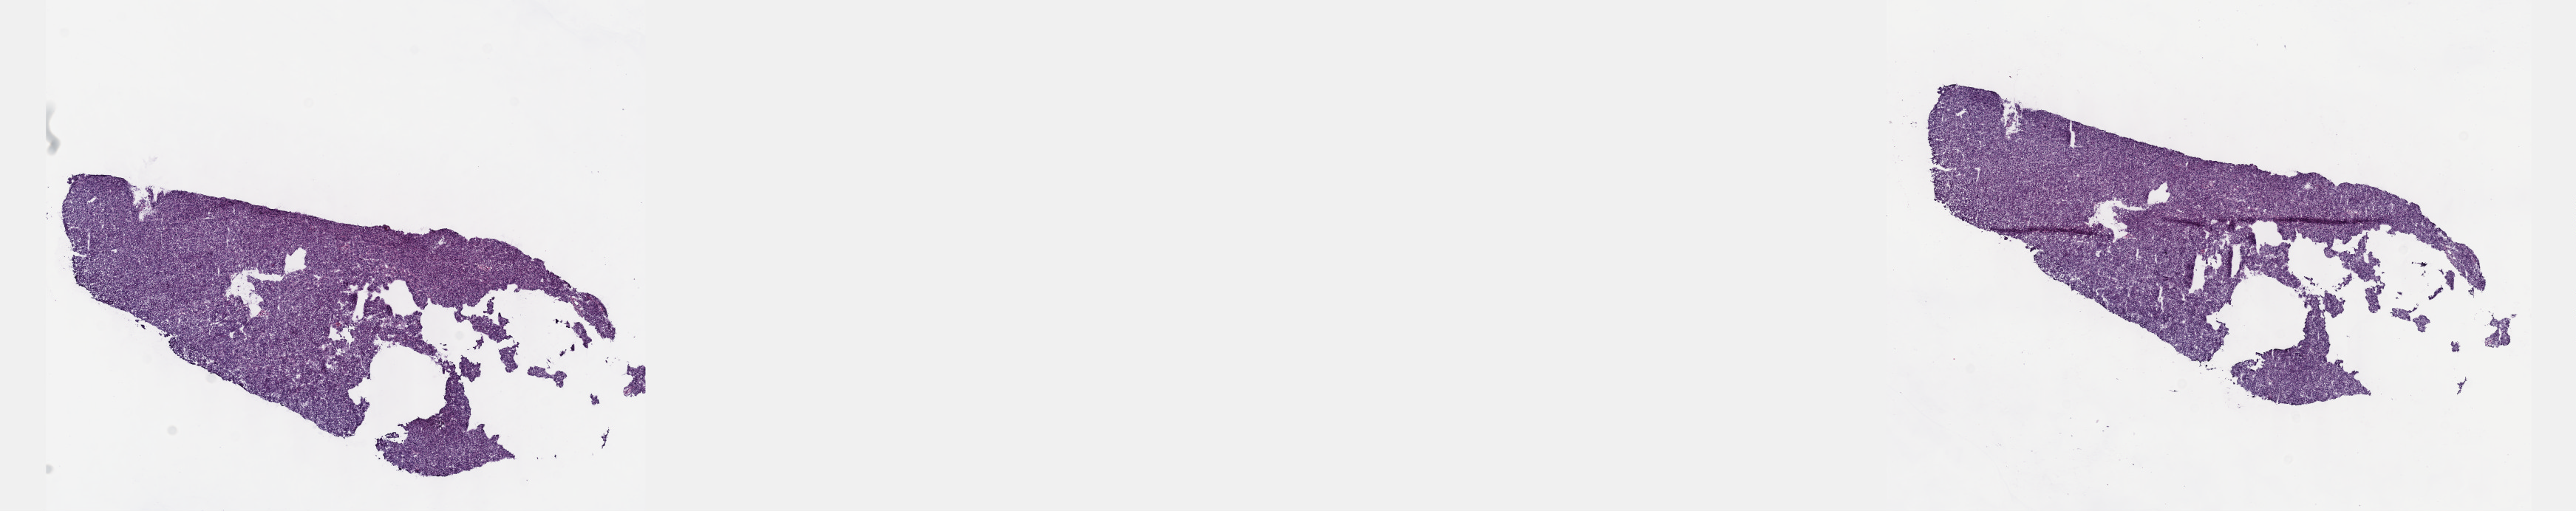
Whole-slide histology image, H&E-stained, a low-resolution overview of the entire scanned area, about 28.2 x 5.6 mm; frozen section from the top of the tissue portion; liver, primary tumour sample. Male patient; age at initial diagnosis 52 years. Histologic grade: G3 (poorly differentiated). Pathologist review of this section (percent, as recorded): tumour cells 97%, tumour nuclei 96%, normal cells 0%, stromal cells 2%, necrosis 1%. Inflammatory infiltration, as recorded: lymphocyte infiltration 3%, monocyte infiltration 0%, neutrophil infiltration 0%.
AJCC pathologic stage: I (7th edition). Diagnosis: Hepatocellular carcinoma, NOS.